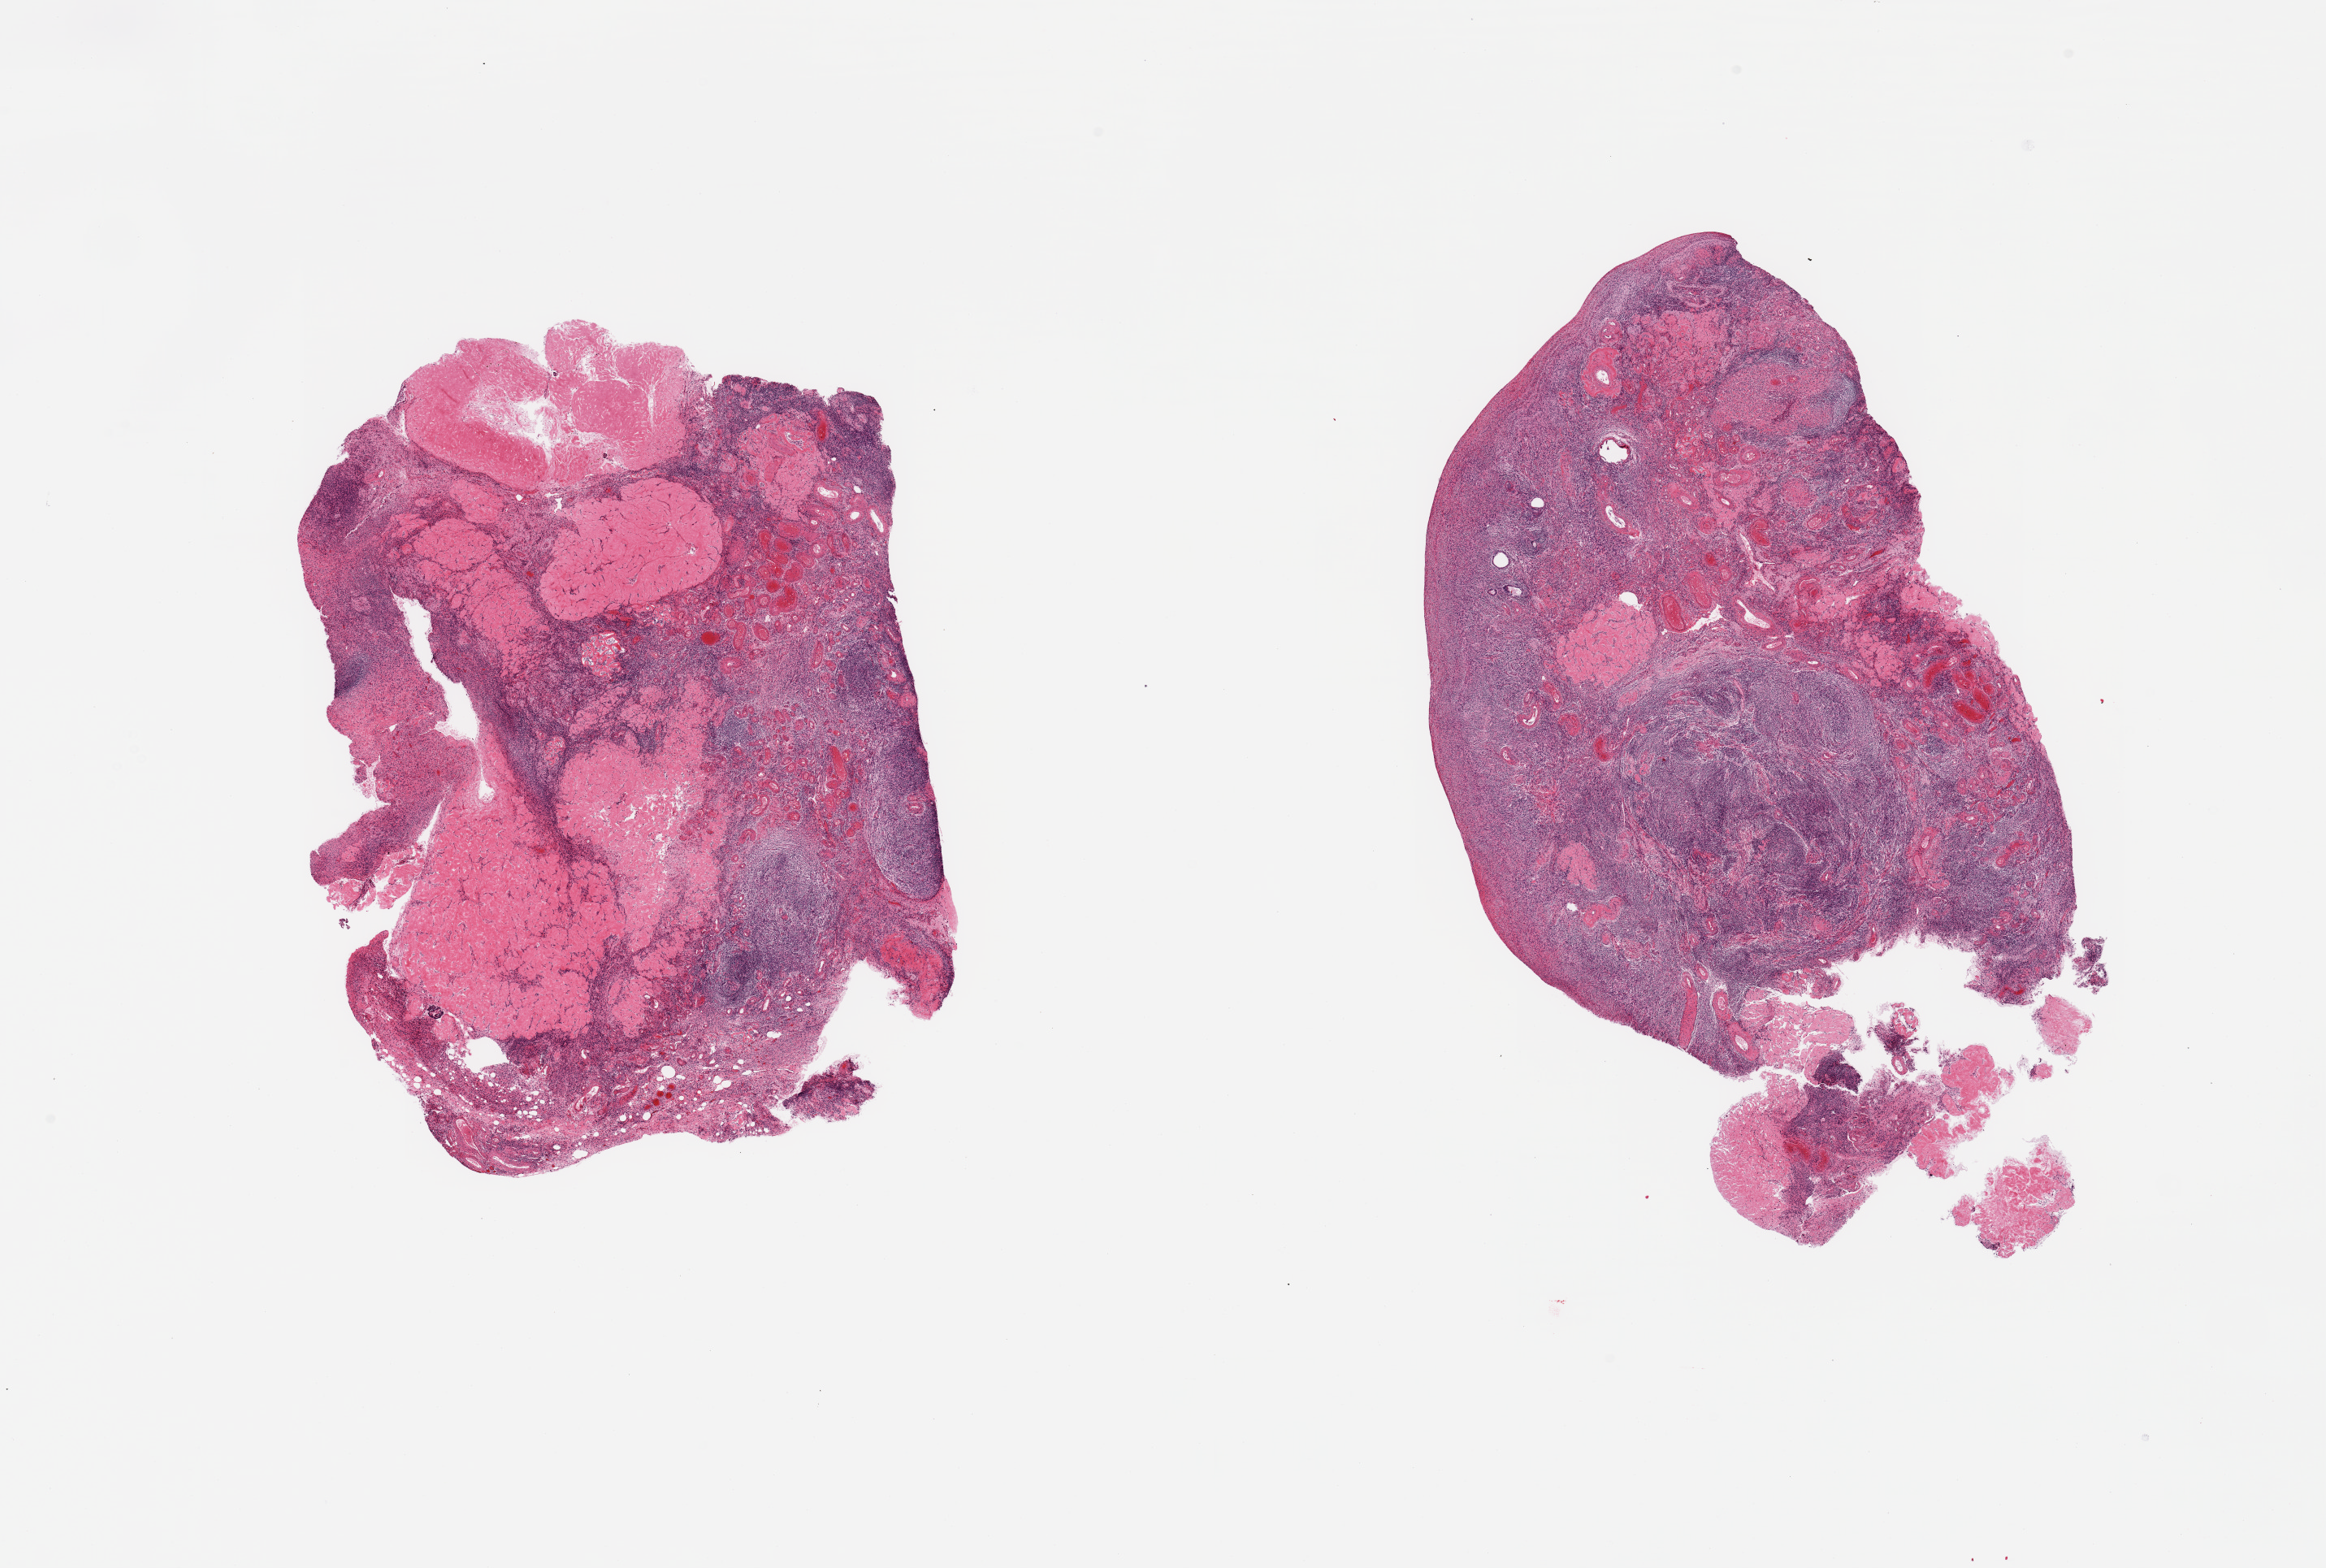
Haematoxylin and eosin whole-slide image — a low-resolution overview of the entire scanned area, about 22.6 x 15.3 mm, PAXgene-fixed paraffin-embedded (PFPE) section, target tissue: ovary, donor tissue sample. Donor: female.
* pathologist's review note for this sample: 2 pieces; 1 piece has 50% corpora albicantia